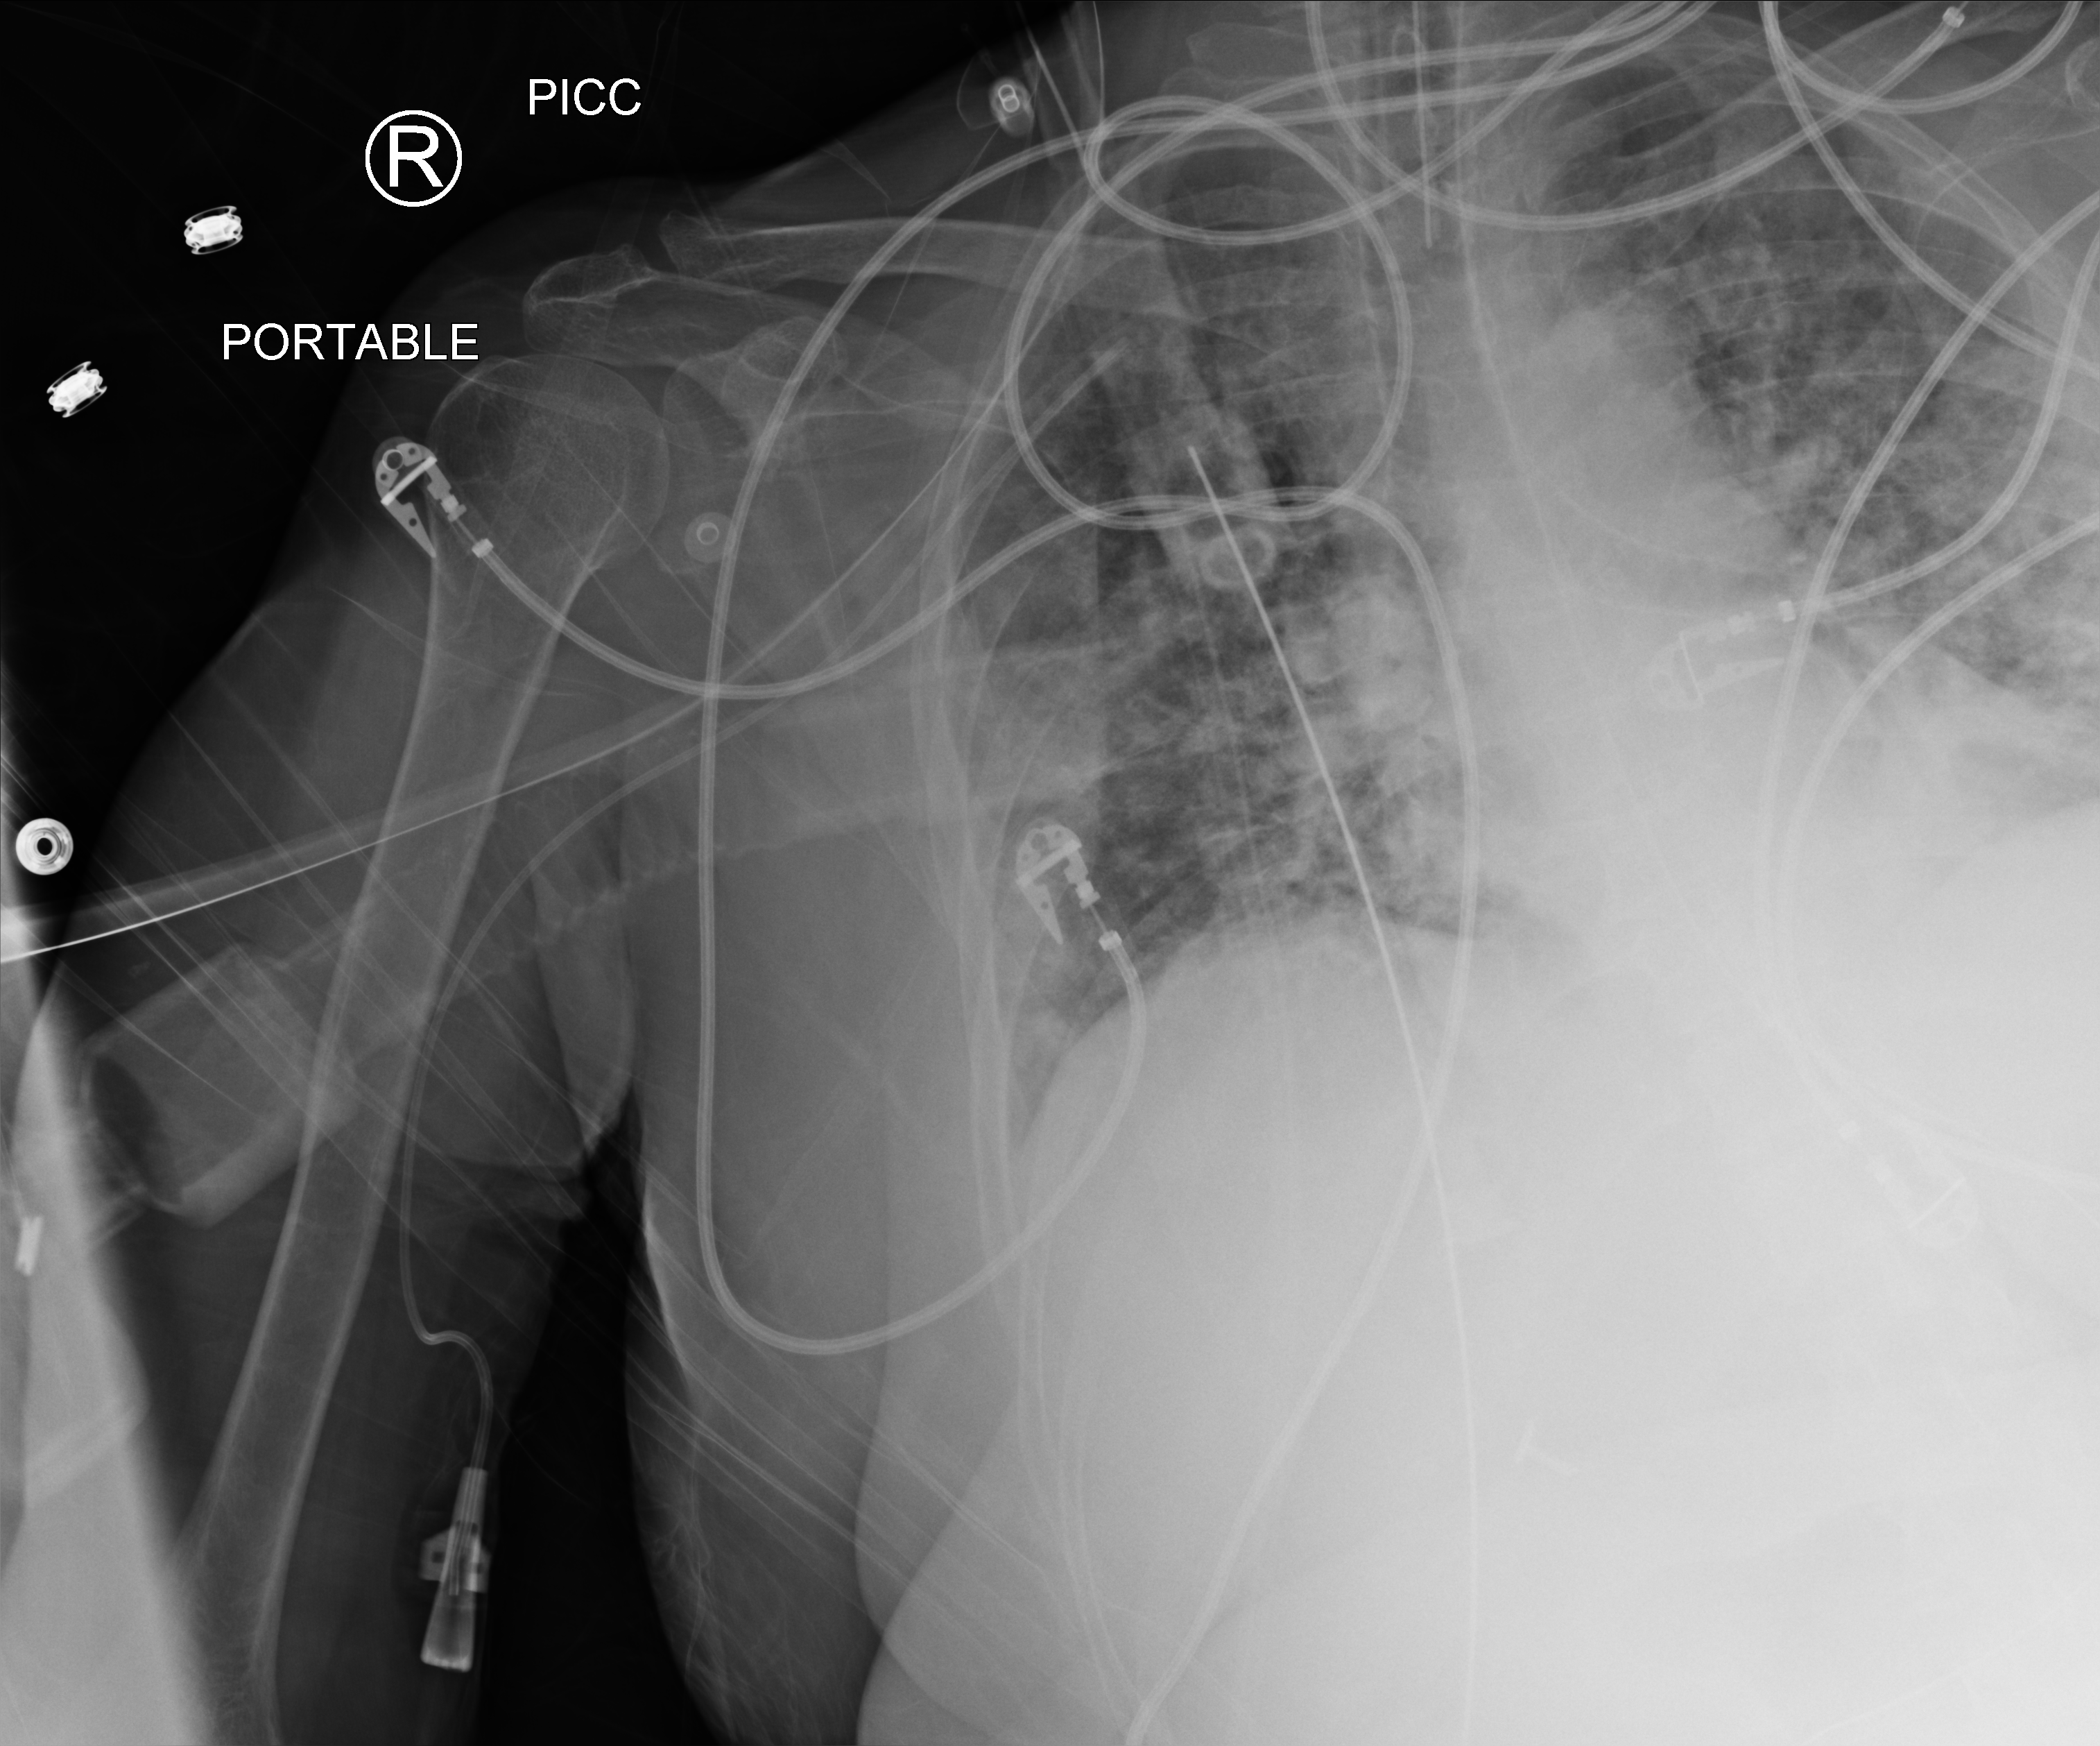
Bedside chest radiograph (computed radiography); anteroposterior (AP) projection. Patient hospitalised with COVID-19; female, aged 18–59 years.
Hospital-stay facts (about this admission, not read from this image; timing relative to this image not recorded): diabetes (admission record): yes; mechanically ventilated during this hospital stay: yes; chronic kidney disease (admission record): yes.